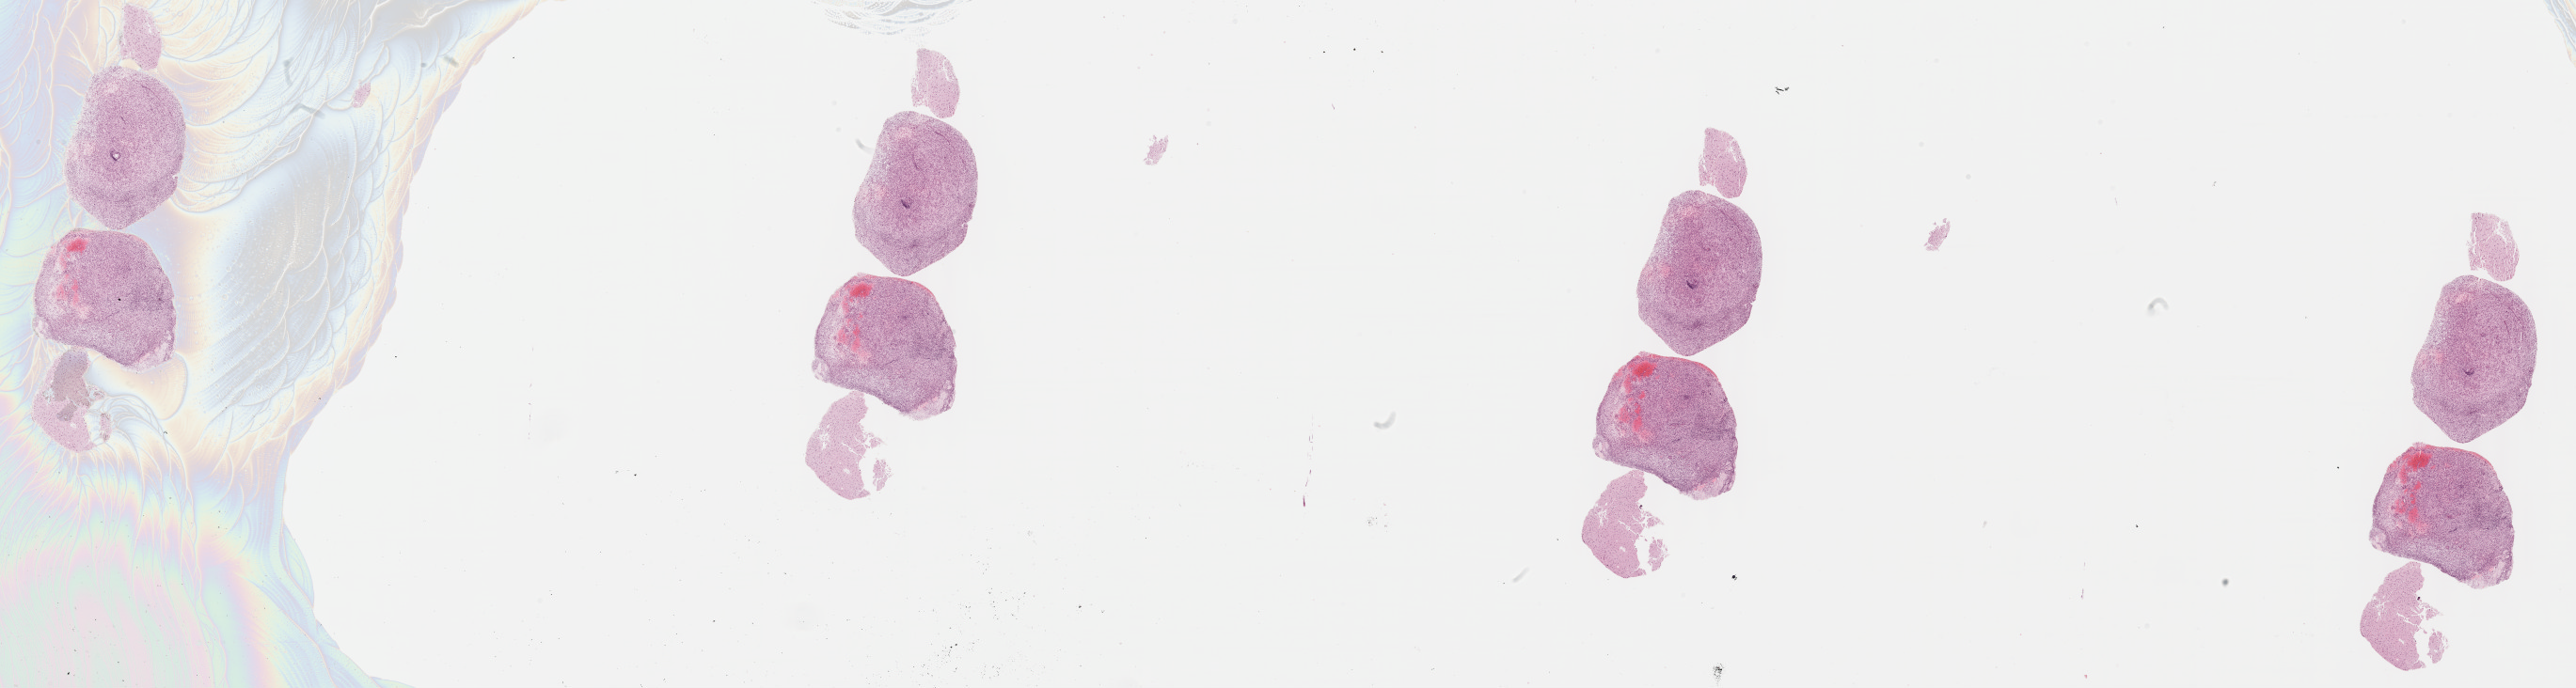
Whole-slide histology image, Hematoxylin and eosin (H&E) stained — whole scanned area (about 44.3 x 11.8 mm, acquisition: 40x scan) shown as a low-resolution overview, formalin-fixed paraffin-embedded (FFPE) diagnostic section, brain, primary tumour sample. Female, age 52 years at initial diagnosis.
Diagnosis: Glioblastoma.